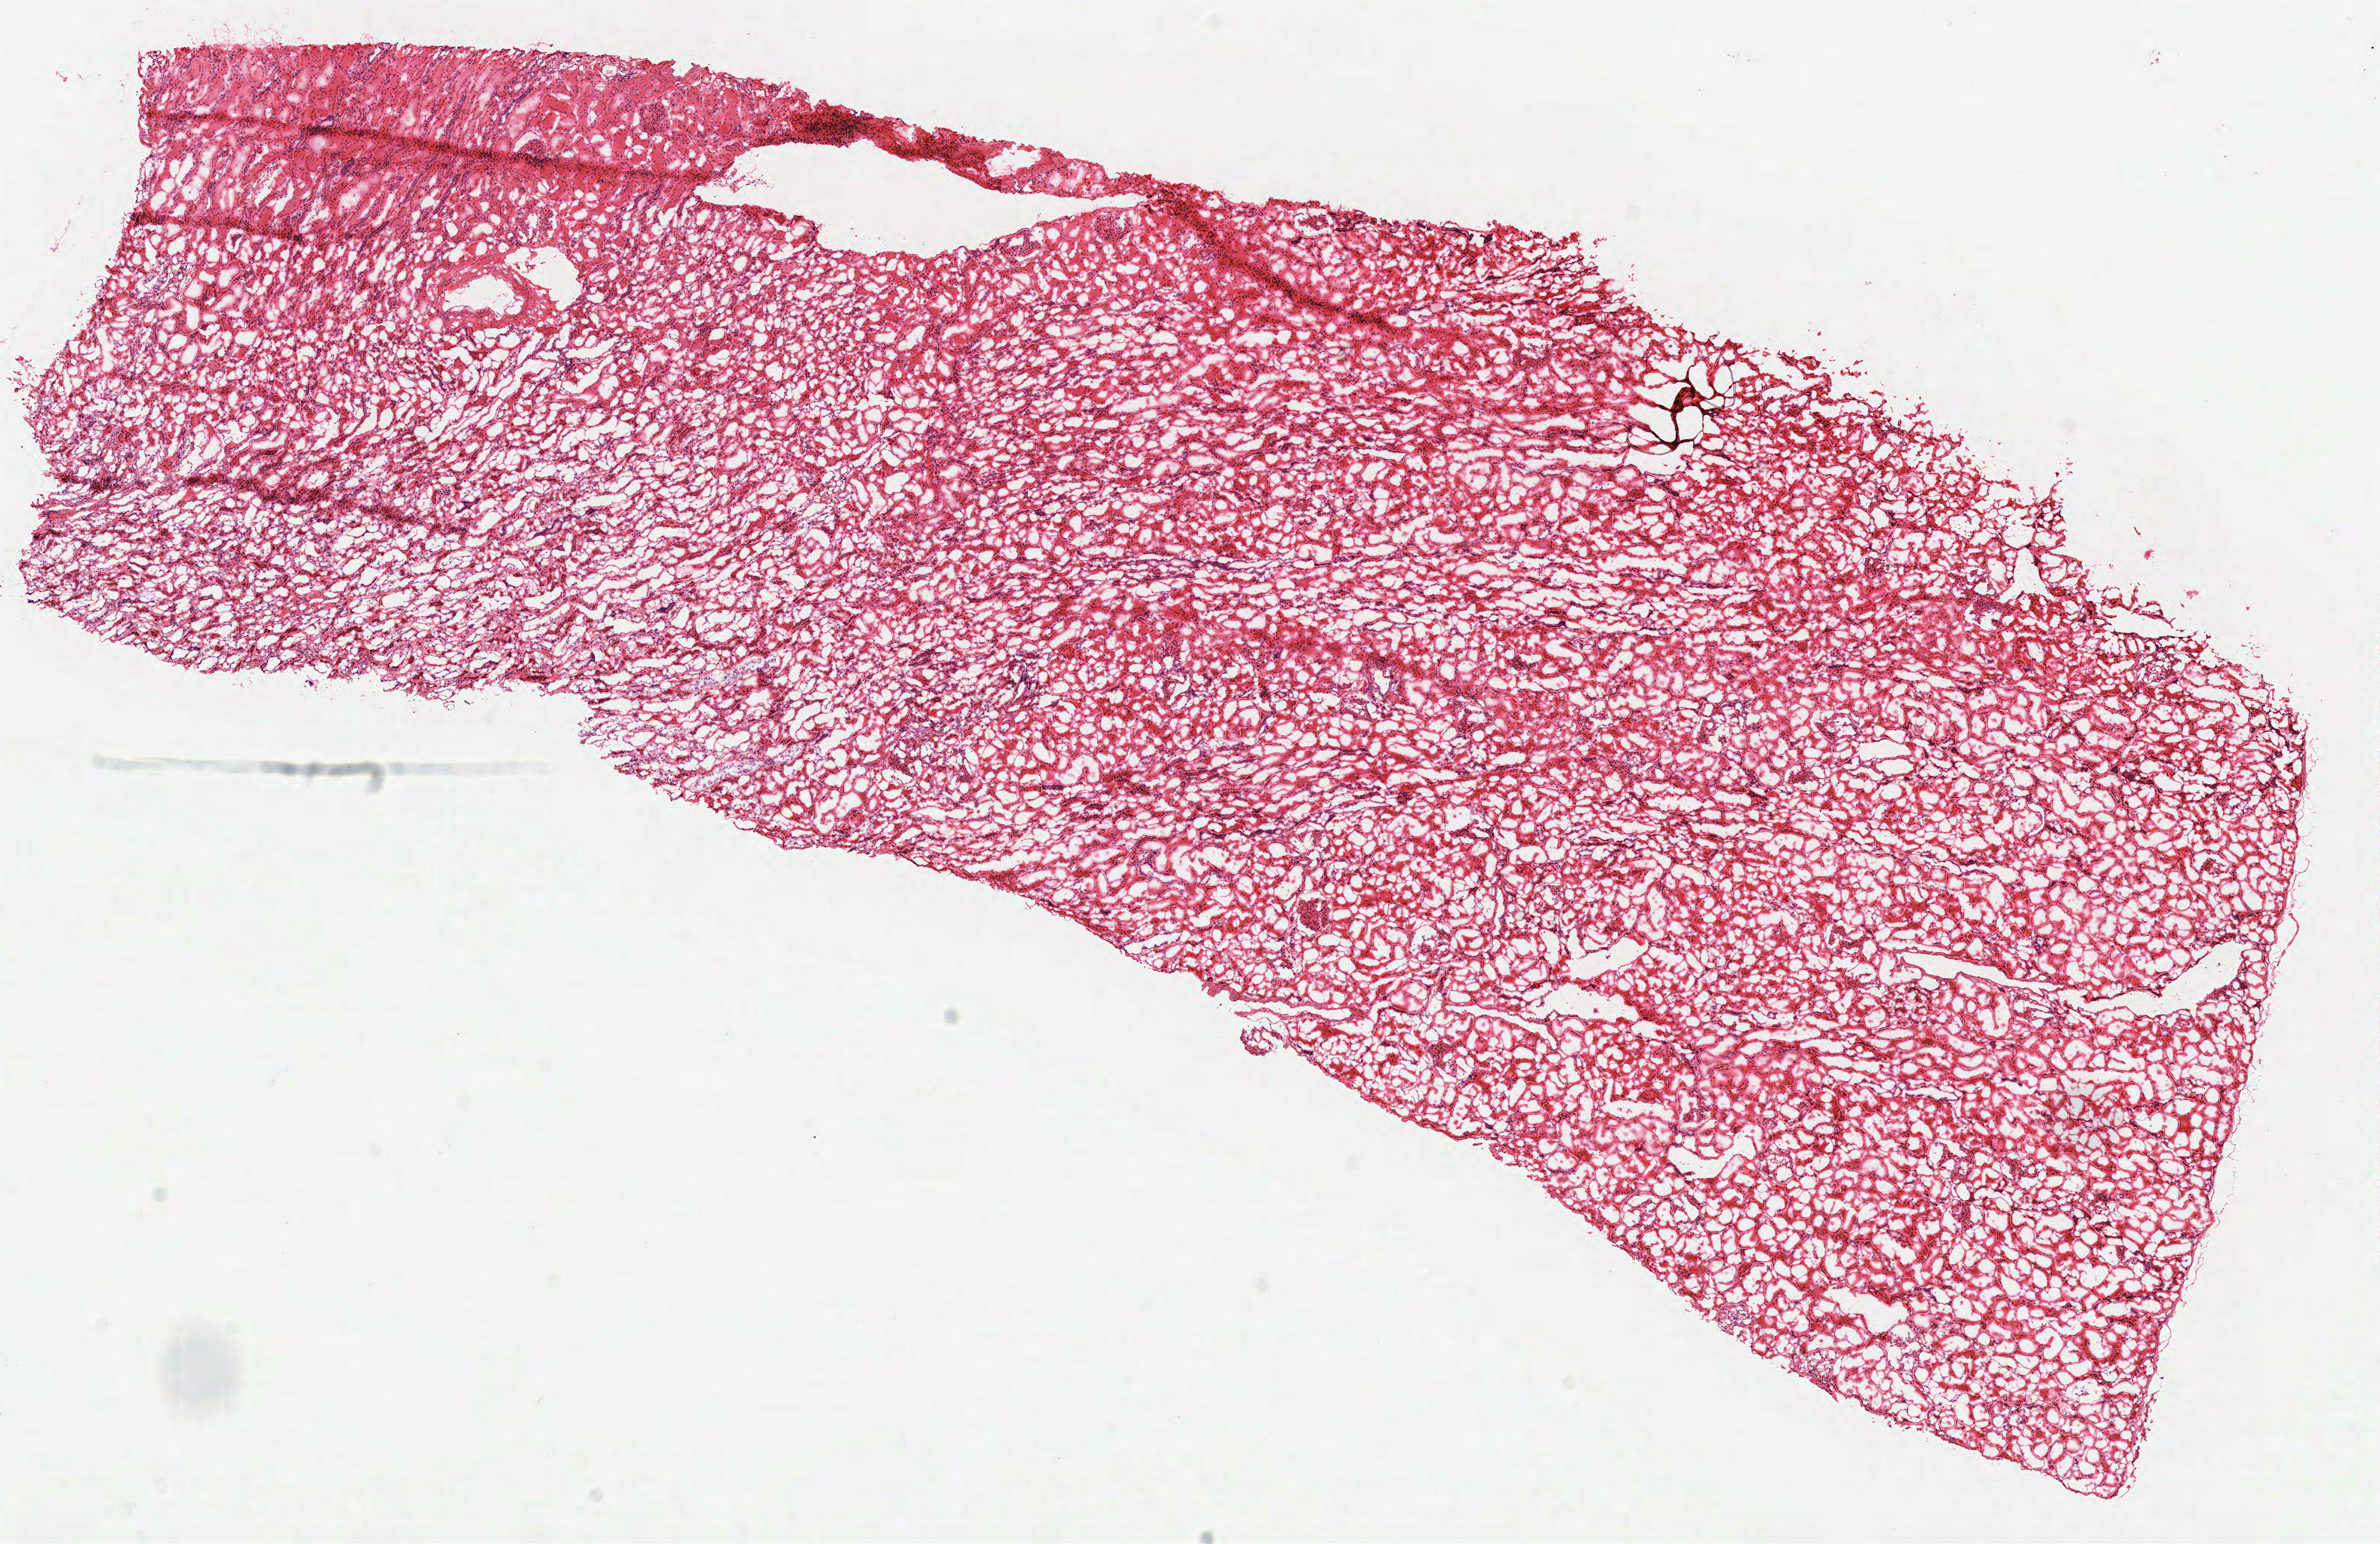
H&E whole-slide image, low-resolution overview of the scanned area, about 12.4 x 8.1 mm (slide scanned at 40x); frozen section from the top of the tissue portion; solid tissue normal (non-tumour tissue) sample from the kidney. Male, age 38 years at initial diagnosis.
This section: solid tissue normal sample (biorepository sample class). Patient diagnosis: Clear cell adenocarcinoma, NOS.